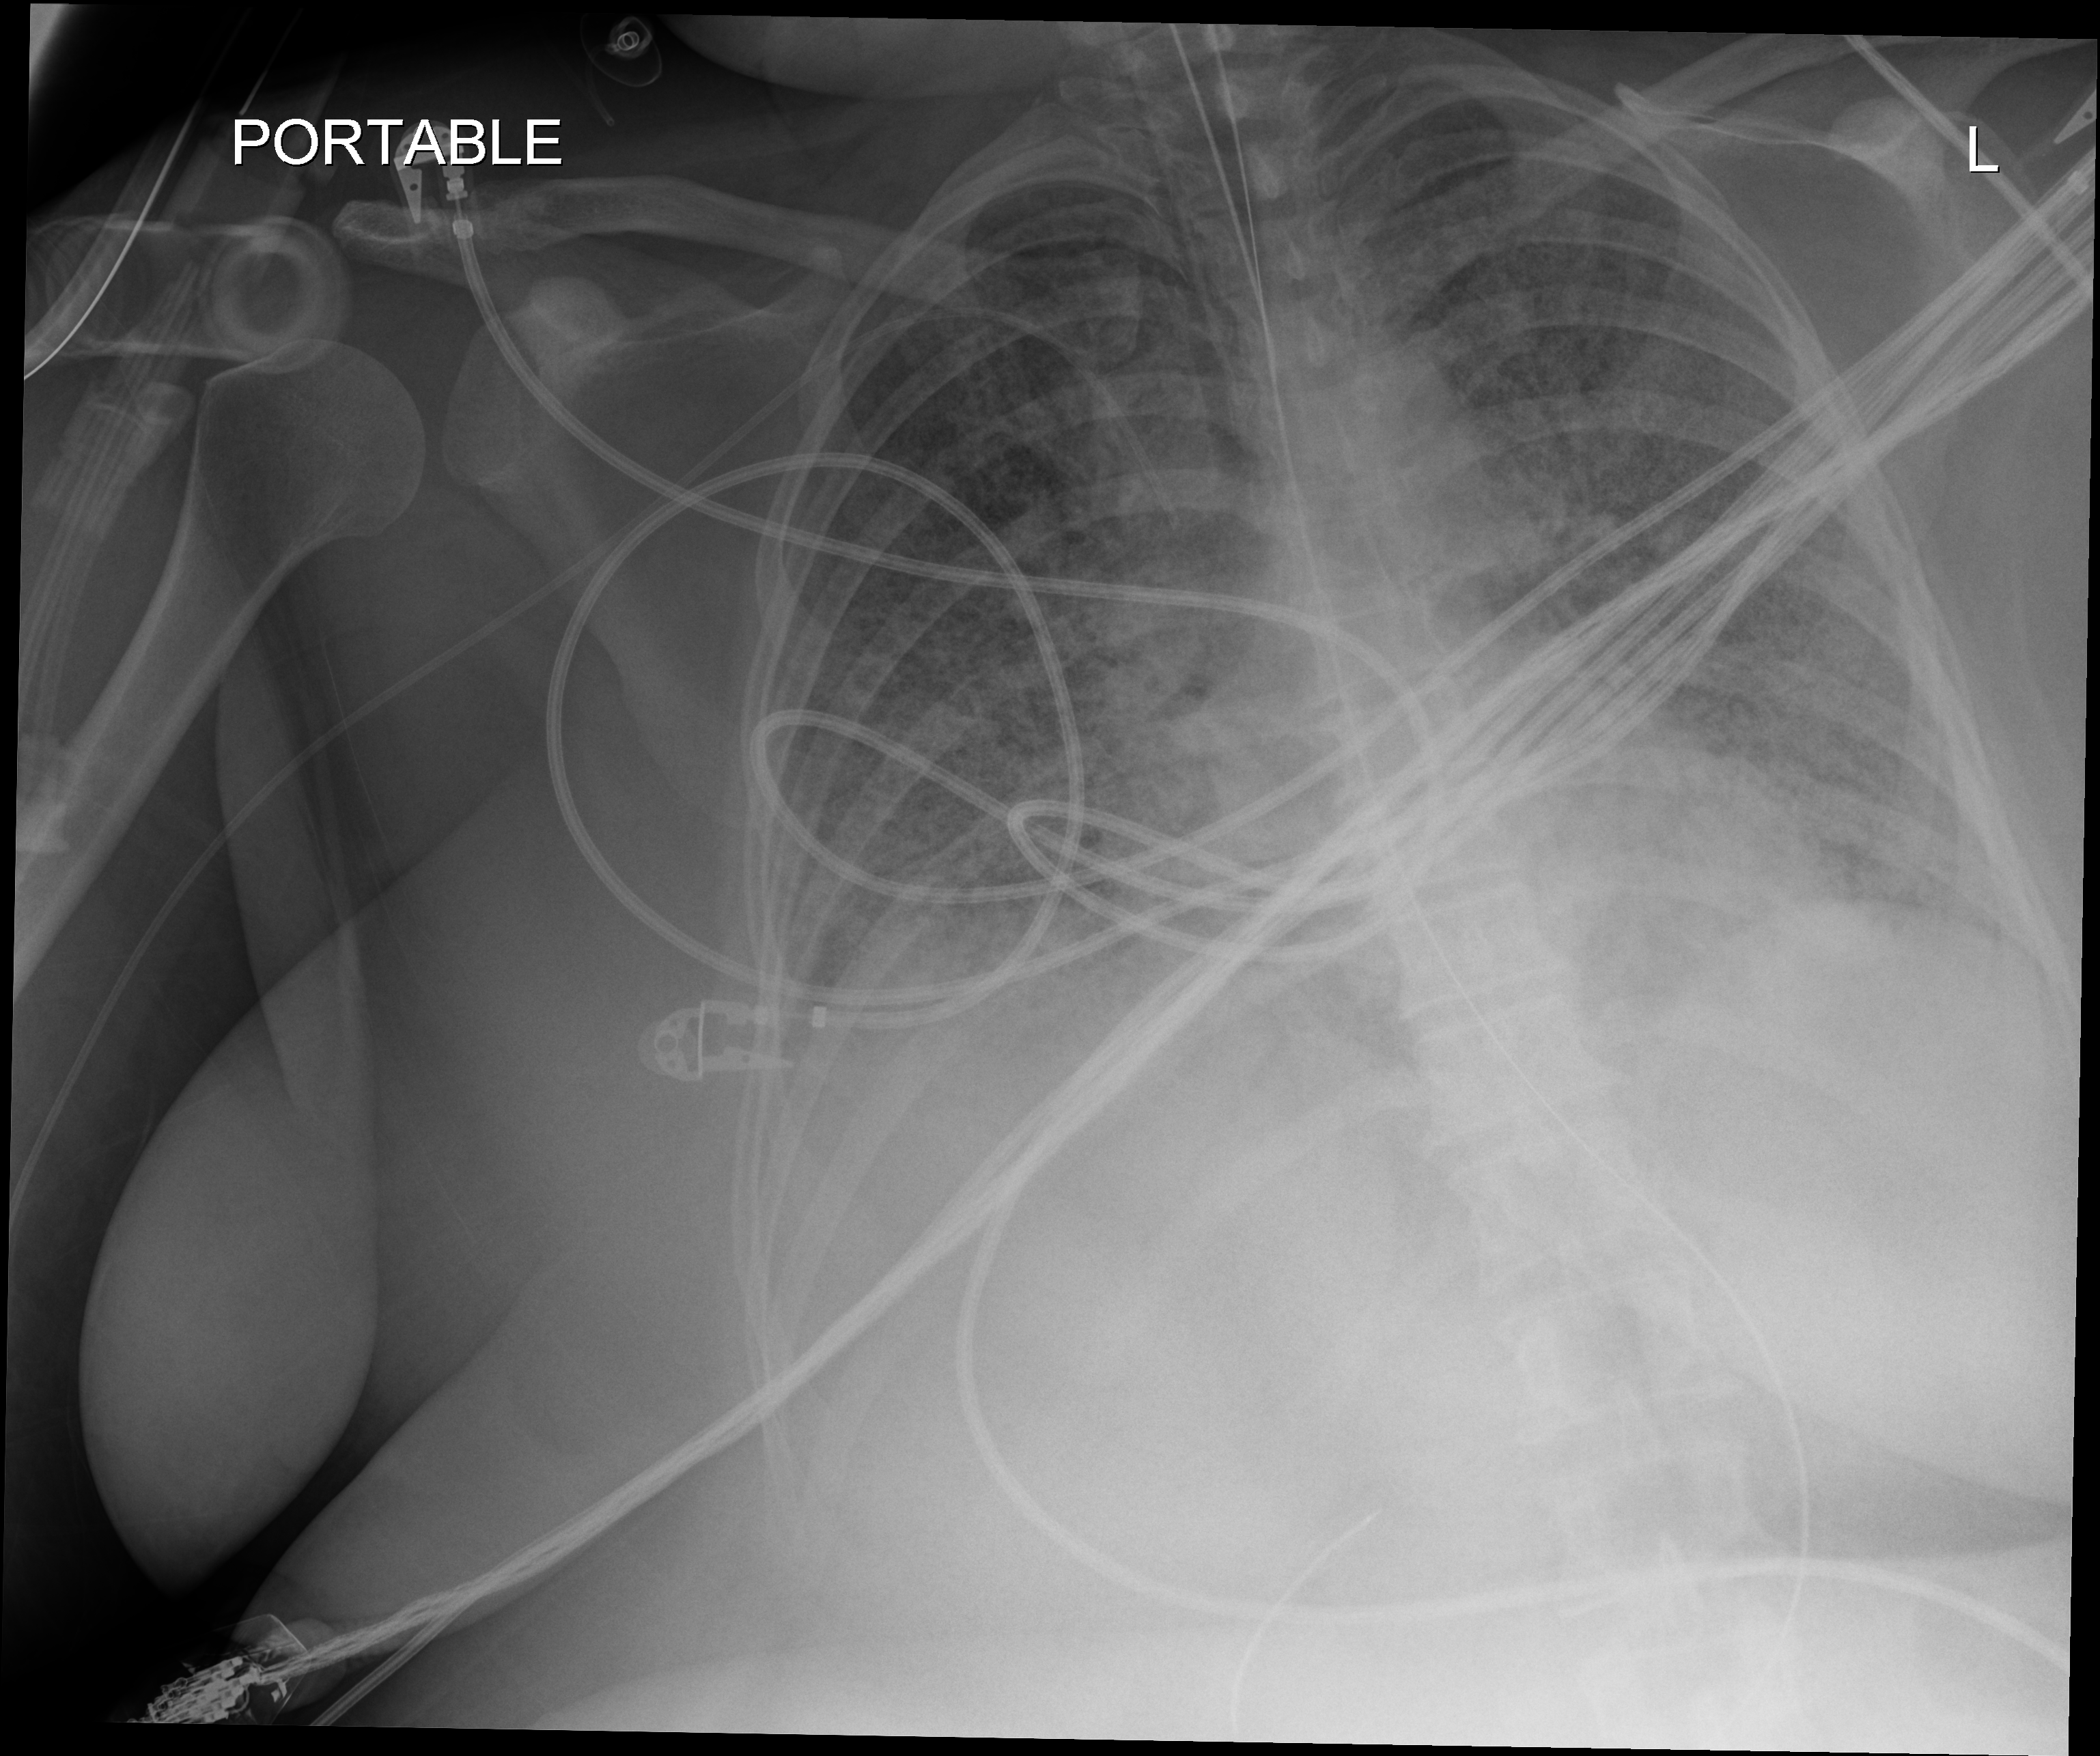
Chest X-ray (portable); anteroposterior (AP) projection. Female patient hospitalised with COVID-19, age 18–59 years.
Hospital-stay facts (about this admission, not read from this image; timing relative to this image not recorded): admitted to intensive care during this hospital stay: yes; mechanically ventilated during this hospital stay: yes.